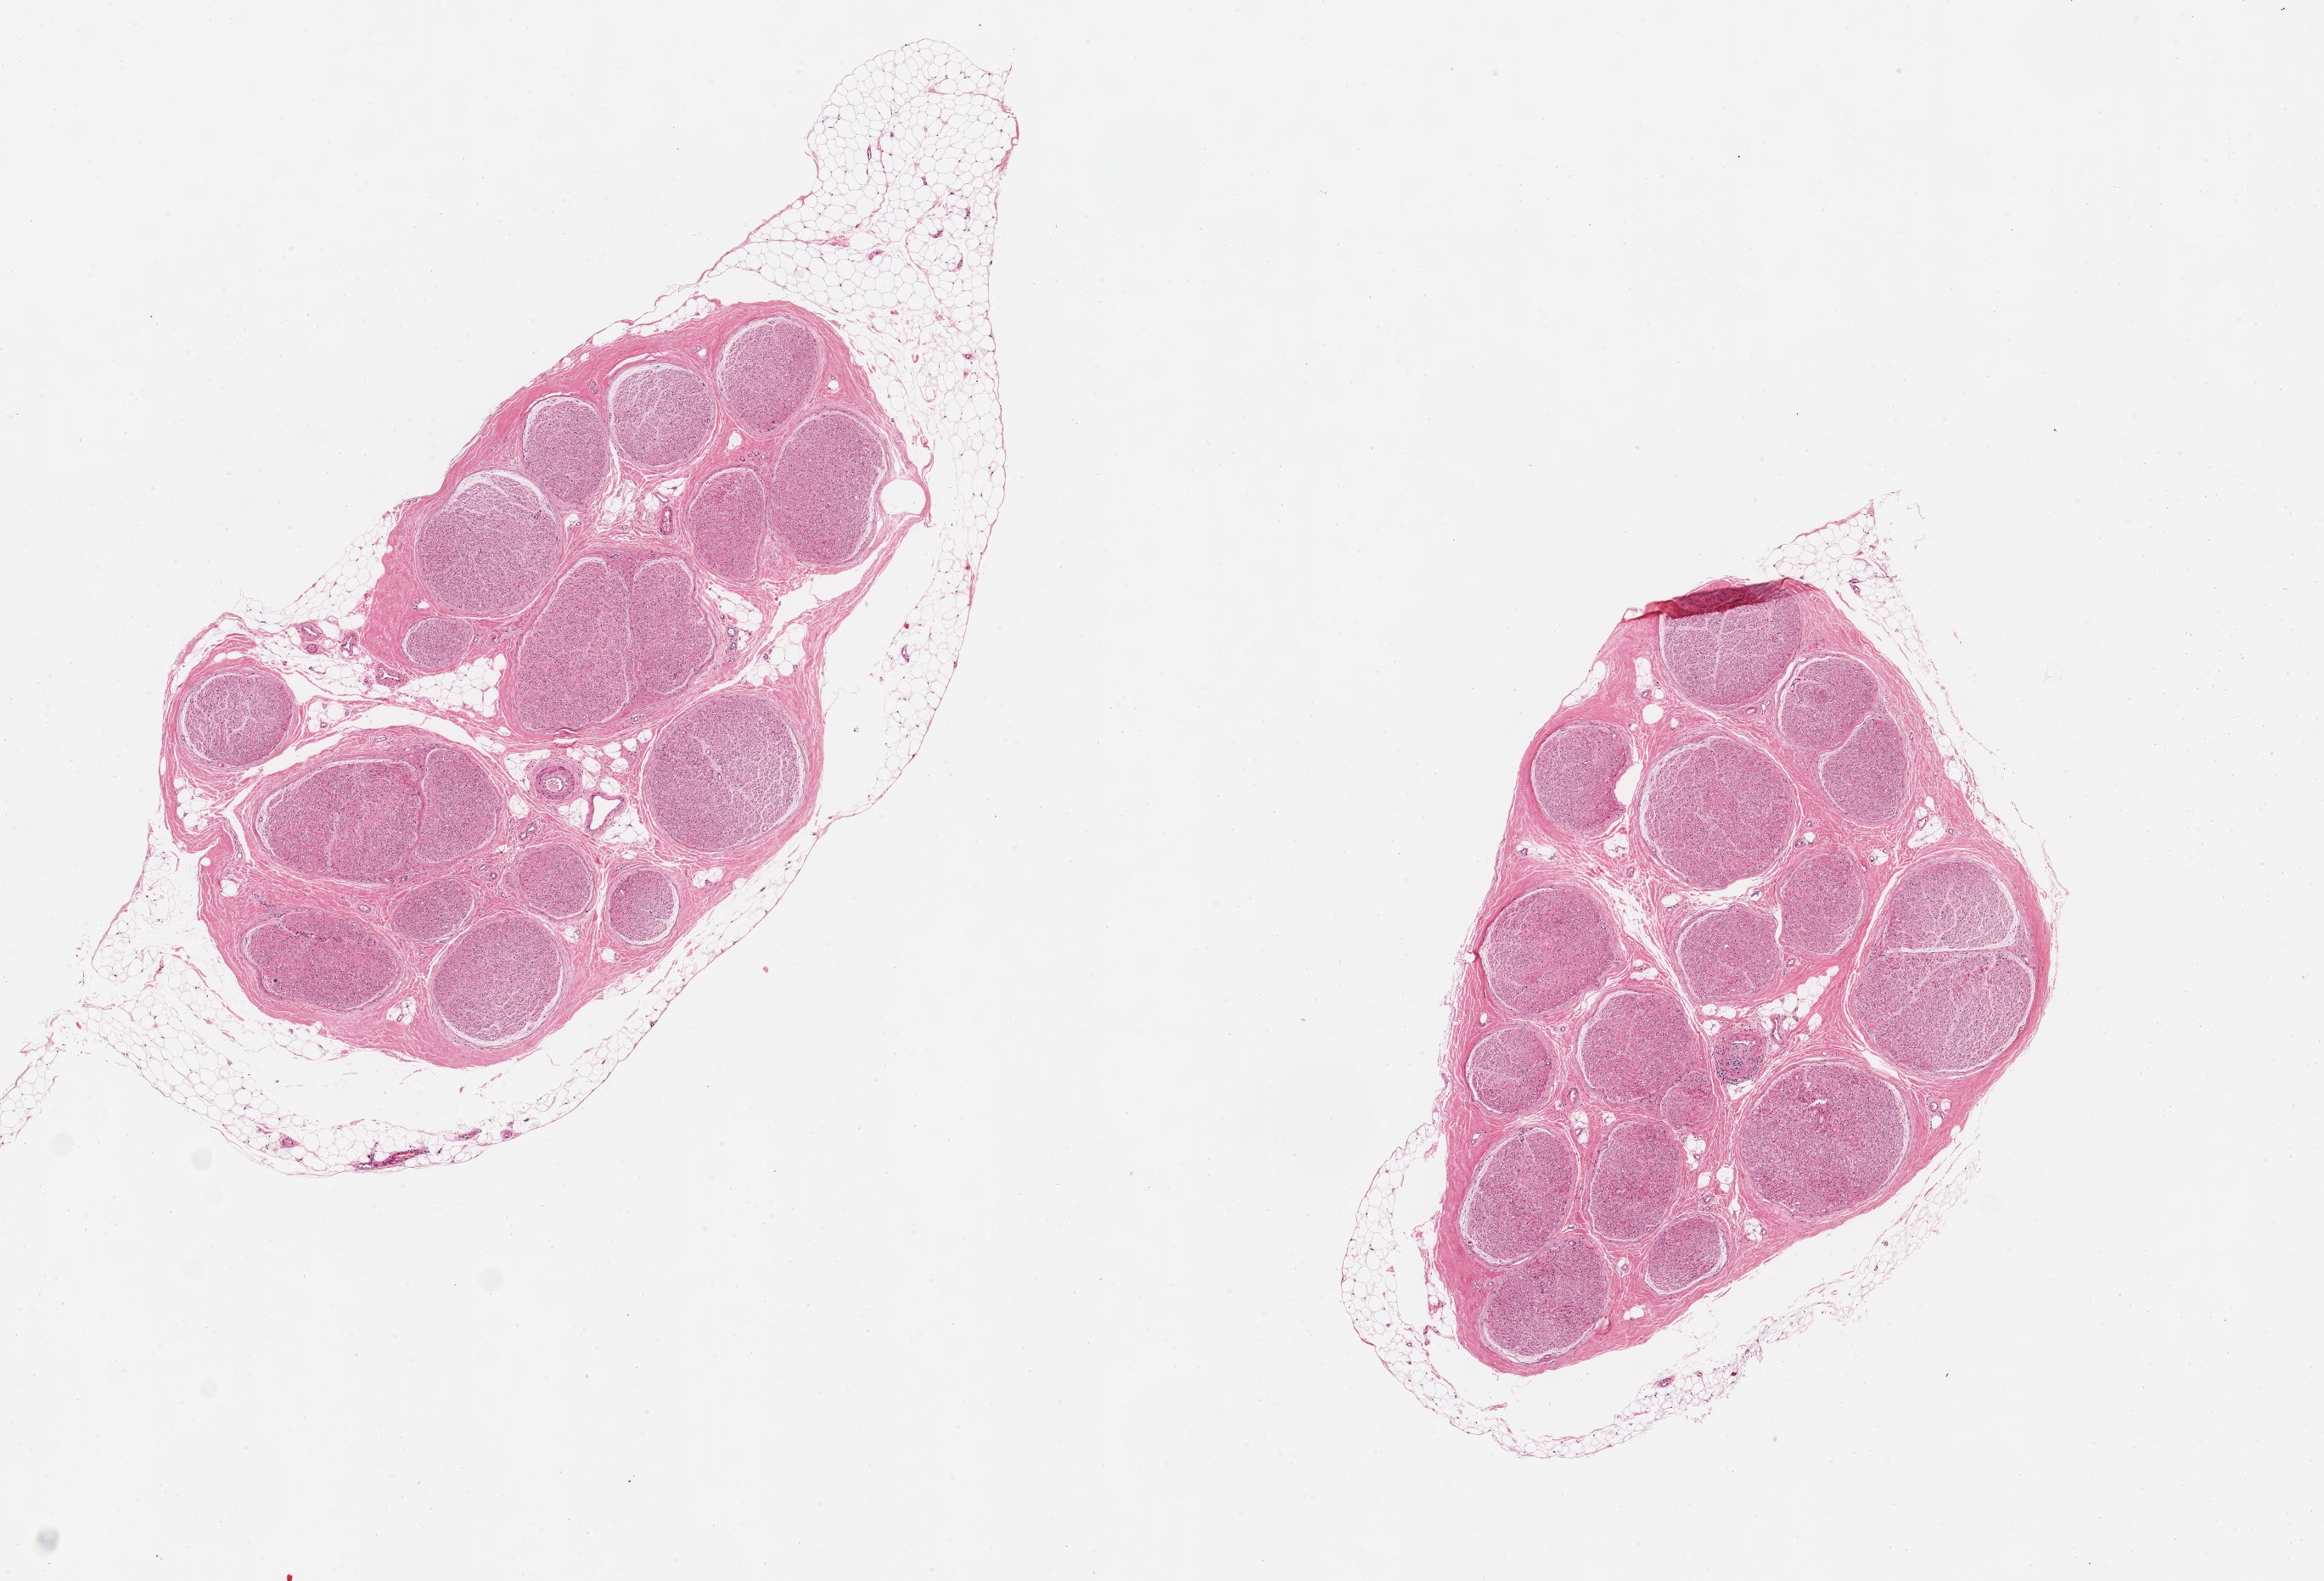
Hematoxylin and eosin (H&E) whole-slide image — shown as a low-resolution overview of the whole scanned area (about 10.8 x 7.4 mm). PAXgene-fixed, paraffin-embedded tissue. Target tissue: tibial nerve. Donor tissue sample. Donor sex: female.
- review note (as recorded): 2 pieces, 6x3 & 4x3 mm; 1 has ~30% adipose